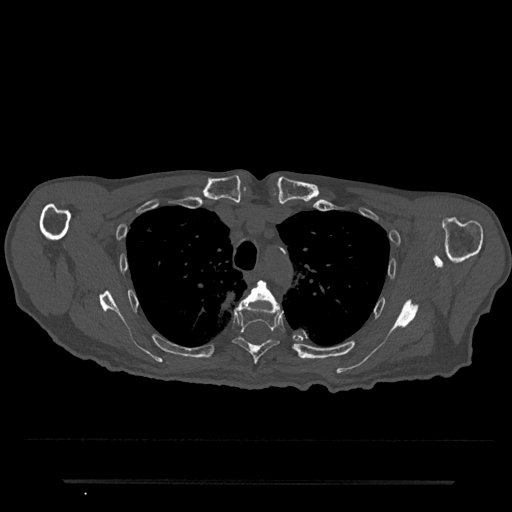
CT including the spine, one axial slice; reconstruction kernel Br40s/3; bone window (W 1800 / L 400 HU); 0.5 mm slice thickness; 512 × 512 image matrix. Patient: male, 74 years. Case-level facts recorded for this patient, not image findings: primary cancer: prostate.
Annotated regions visible in this slice (semi-automatically segmented with operator editing):
- T4 vertebra: bounding box <246,280,277,304> (left, top, right, bottom; pixels)
- T5 vertebra: <233,298,282,365>